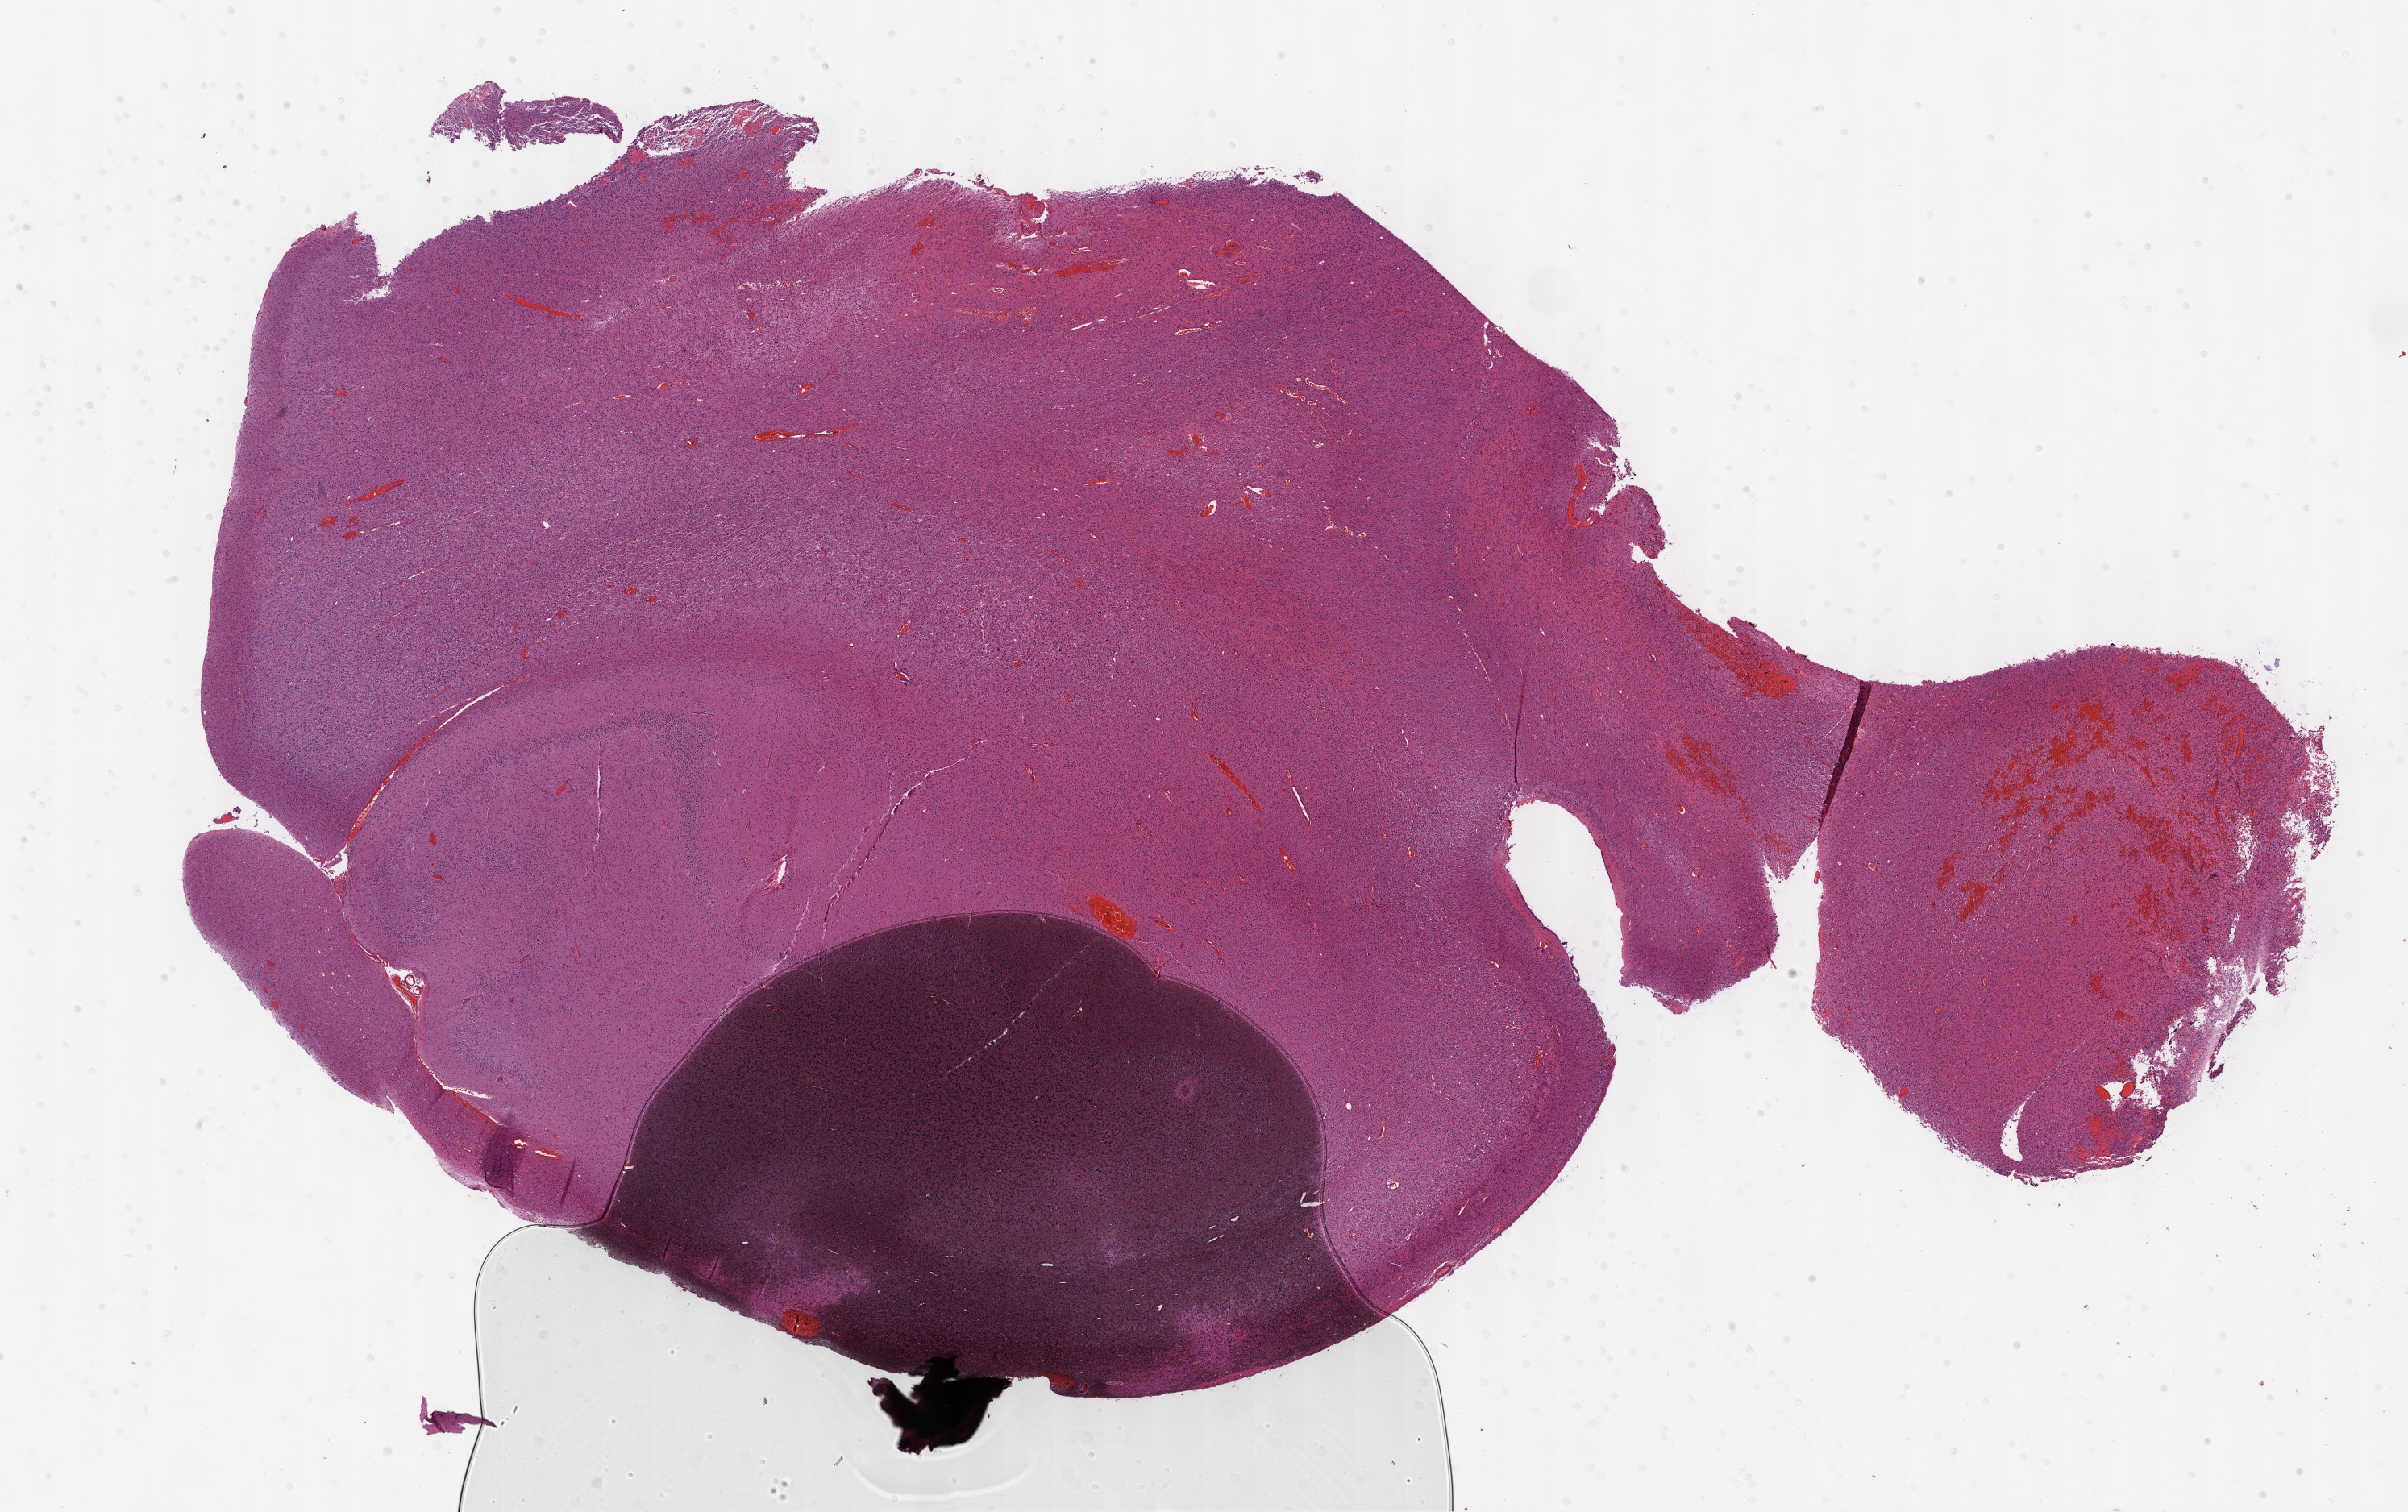
H&E whole-slide image — a low-resolution overview of the entire scanned area, about 24.2 x 15.2 mm. FFPE section. Brain, primary tumour sample. Male patient; age at initial diagnosis 37 years. Histologic grade: G3 (poorly differentiated).
Histologic diagnosis: Oligodendroglioma, anaplastic. Laterality: right.